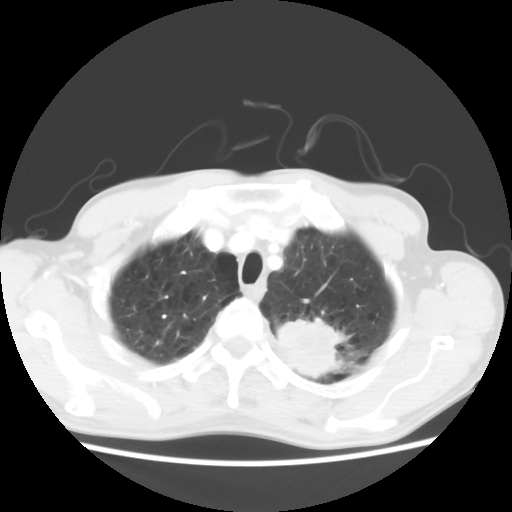
Chest CT, one axial slice. Position 54 of 64 along the scan axis. Reconstruction kernel STANDARD. 120 kVp. Lung window (W 1500 / L -600 HU). 512 × 512 image matrix, field of view 346 × 346 mm. Male patient, age 63 years. Case-level facts recorded for this patient, not image findings: clinical TNM (as recorded): T2 N0 M0.
Annotated regions visible in this slice (rectangle marked by the reading radiologist):
- lung tumour (recorded histology: adenocarcinoma): bounding box <275,311,350,383> (left, top, right, bottom; pixels)